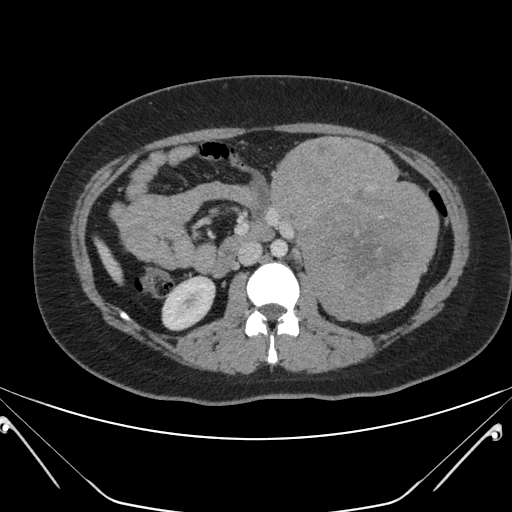
Contrast-enhanced abdominal CT, one axial slice. Slice 104 of 168 in the series (ordered by position). Intravenous contrast given. Soft-tissue window (W 400 / L 40 HU). 3 mm slice thickness. 512 × 512 image matrix. Female patient, age 26 years. From the clinical record (not read from this slice): diagnosis: adrenocortical carcinoma; tumour side: left adrenal; tumour size at pathology: 28 cm; Ki-67 index: 20 %; stage (as recorded): 2.
Outlined on this slice (semi-automatically segmented with operator editing):
- mass: bounding box <270,136,438,322> (left, top, right, bottom; pixels)